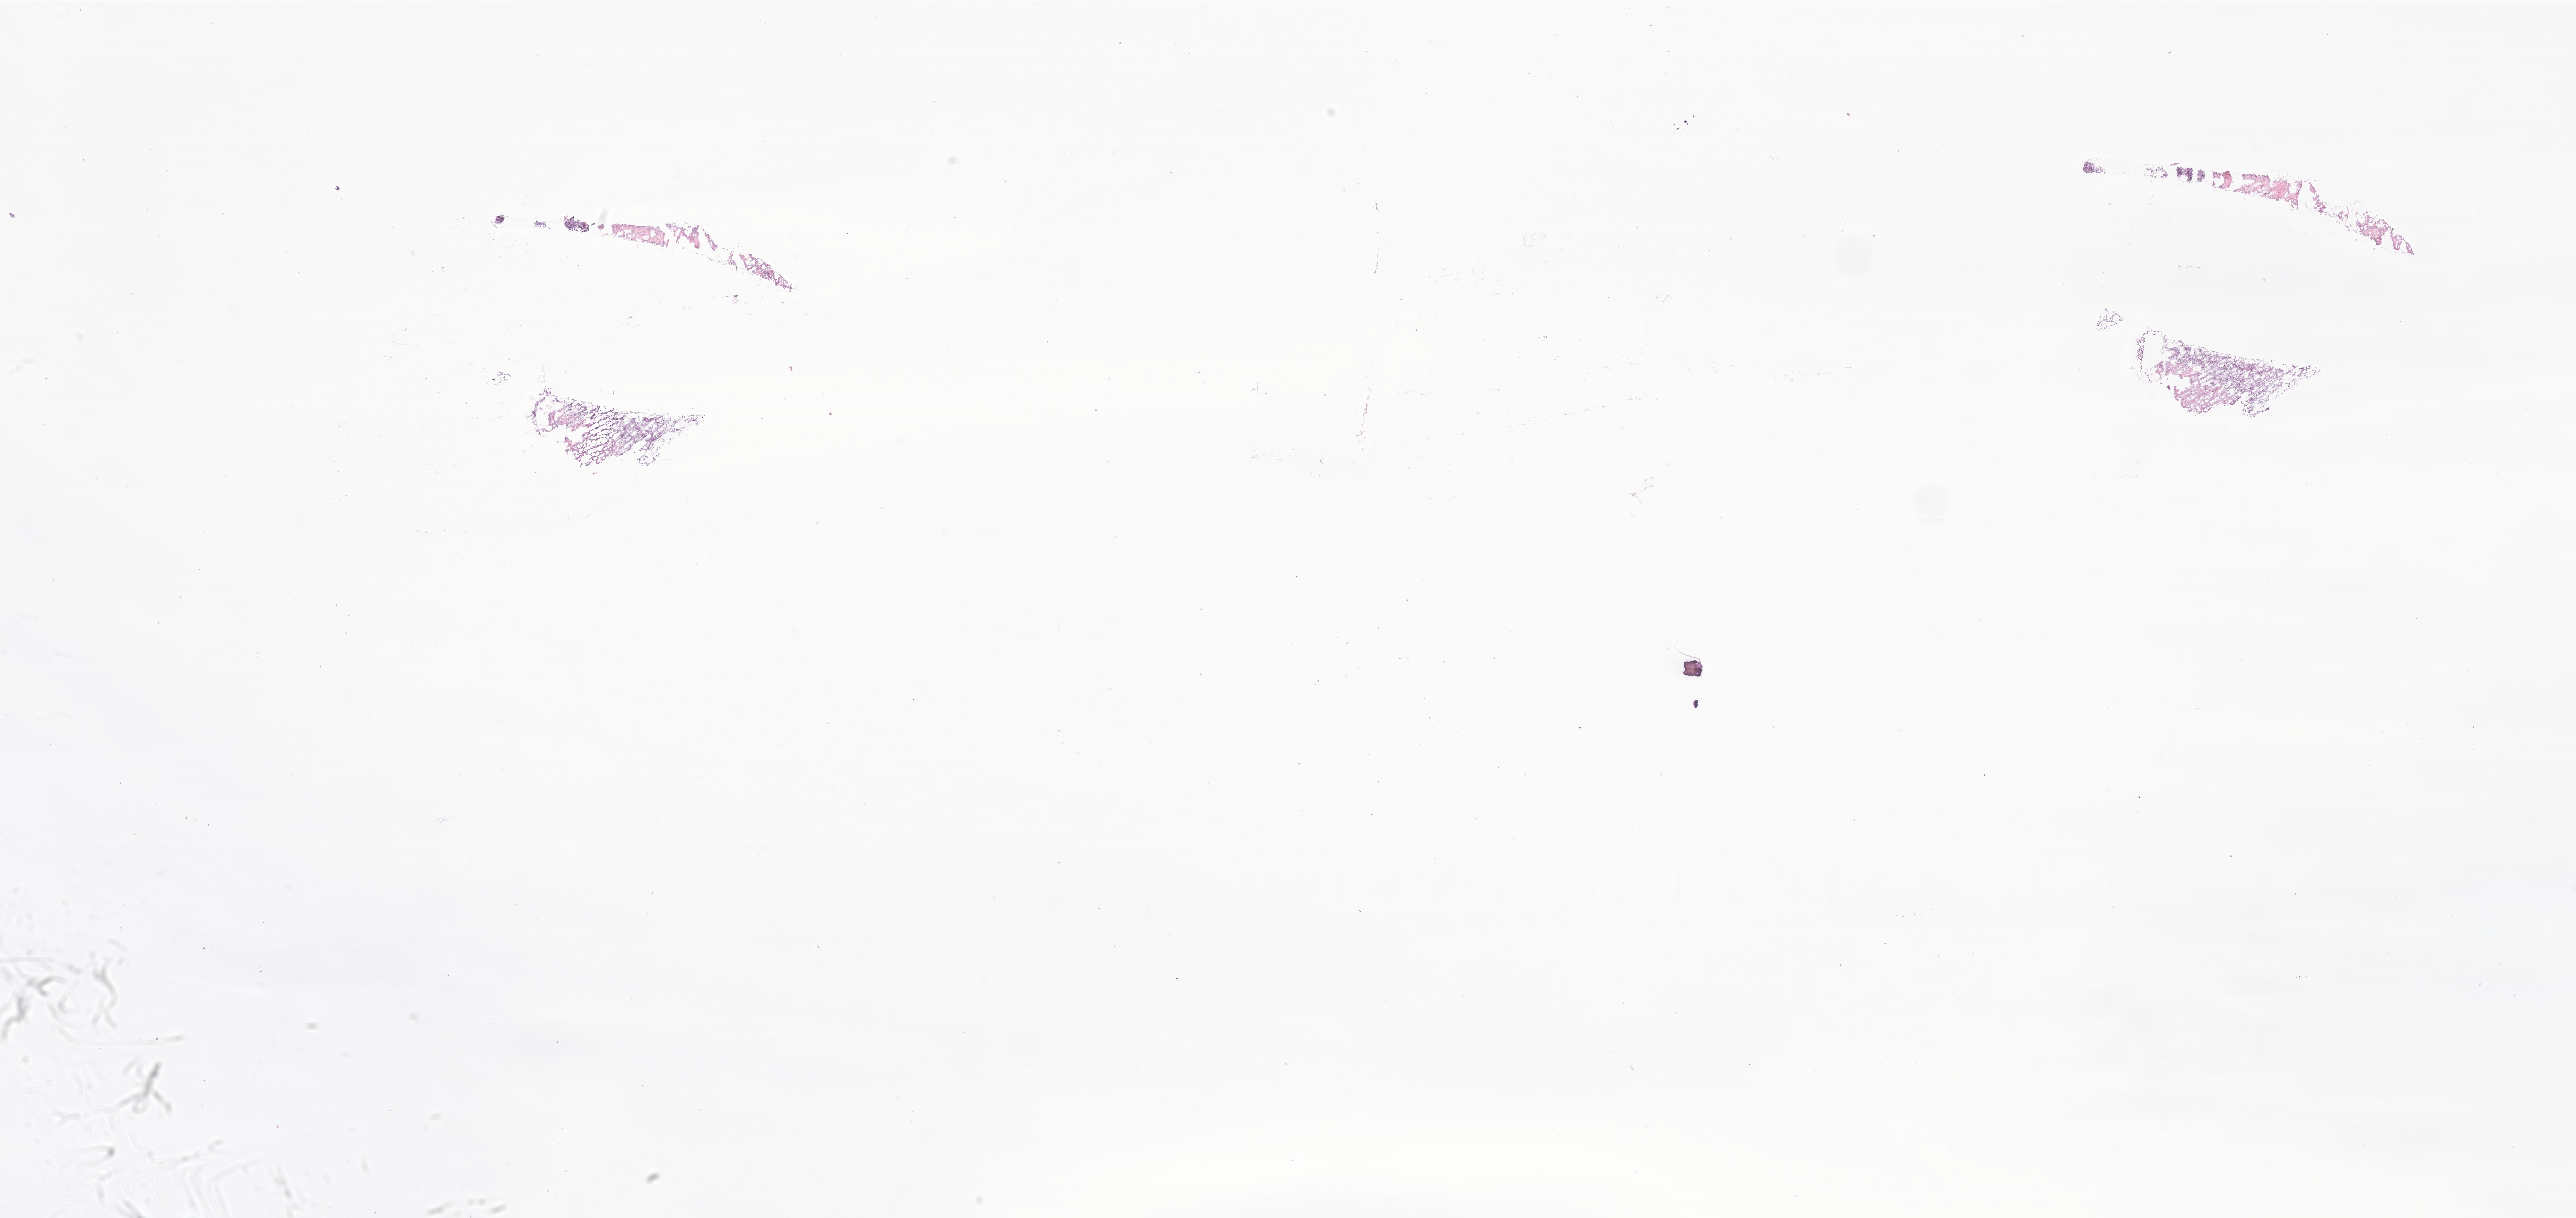
Digitized haematoxylin and eosin-stained section of tumor tissue from the brain — a low-resolution overview of the entire scanned area, about 31.3 x 14.8 mm. Cryosection (OCT / tissue freezing medium). Male patient, age 186 months.
Recorded diagnosis: Pilocytic astrocytoma.